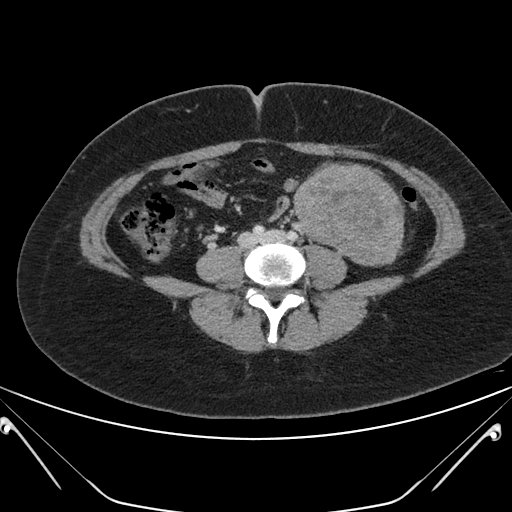
Contrast-enhanced abdominal CT, one axial slice; slice 75 of 168 in the series (ordered by position); 120 kVp; soft-tissue window (W 400 / L 40 HU); 3 mm slice thickness; 512 × 512 image matrix. Patient: female, 26 years. From the clinical record (not read from this slice): diagnosis: adrenocortical carcinoma; tumour side: left adrenal; tumour size at pathology: 28 cm; Ki-67 index: 20 %; stage (as recorded): 2.
Annotated regions visible in this slice (semi-automatically segmented with operator editing):
- mass: bounding box <293,164,403,265> (left, top, right, bottom; pixels)